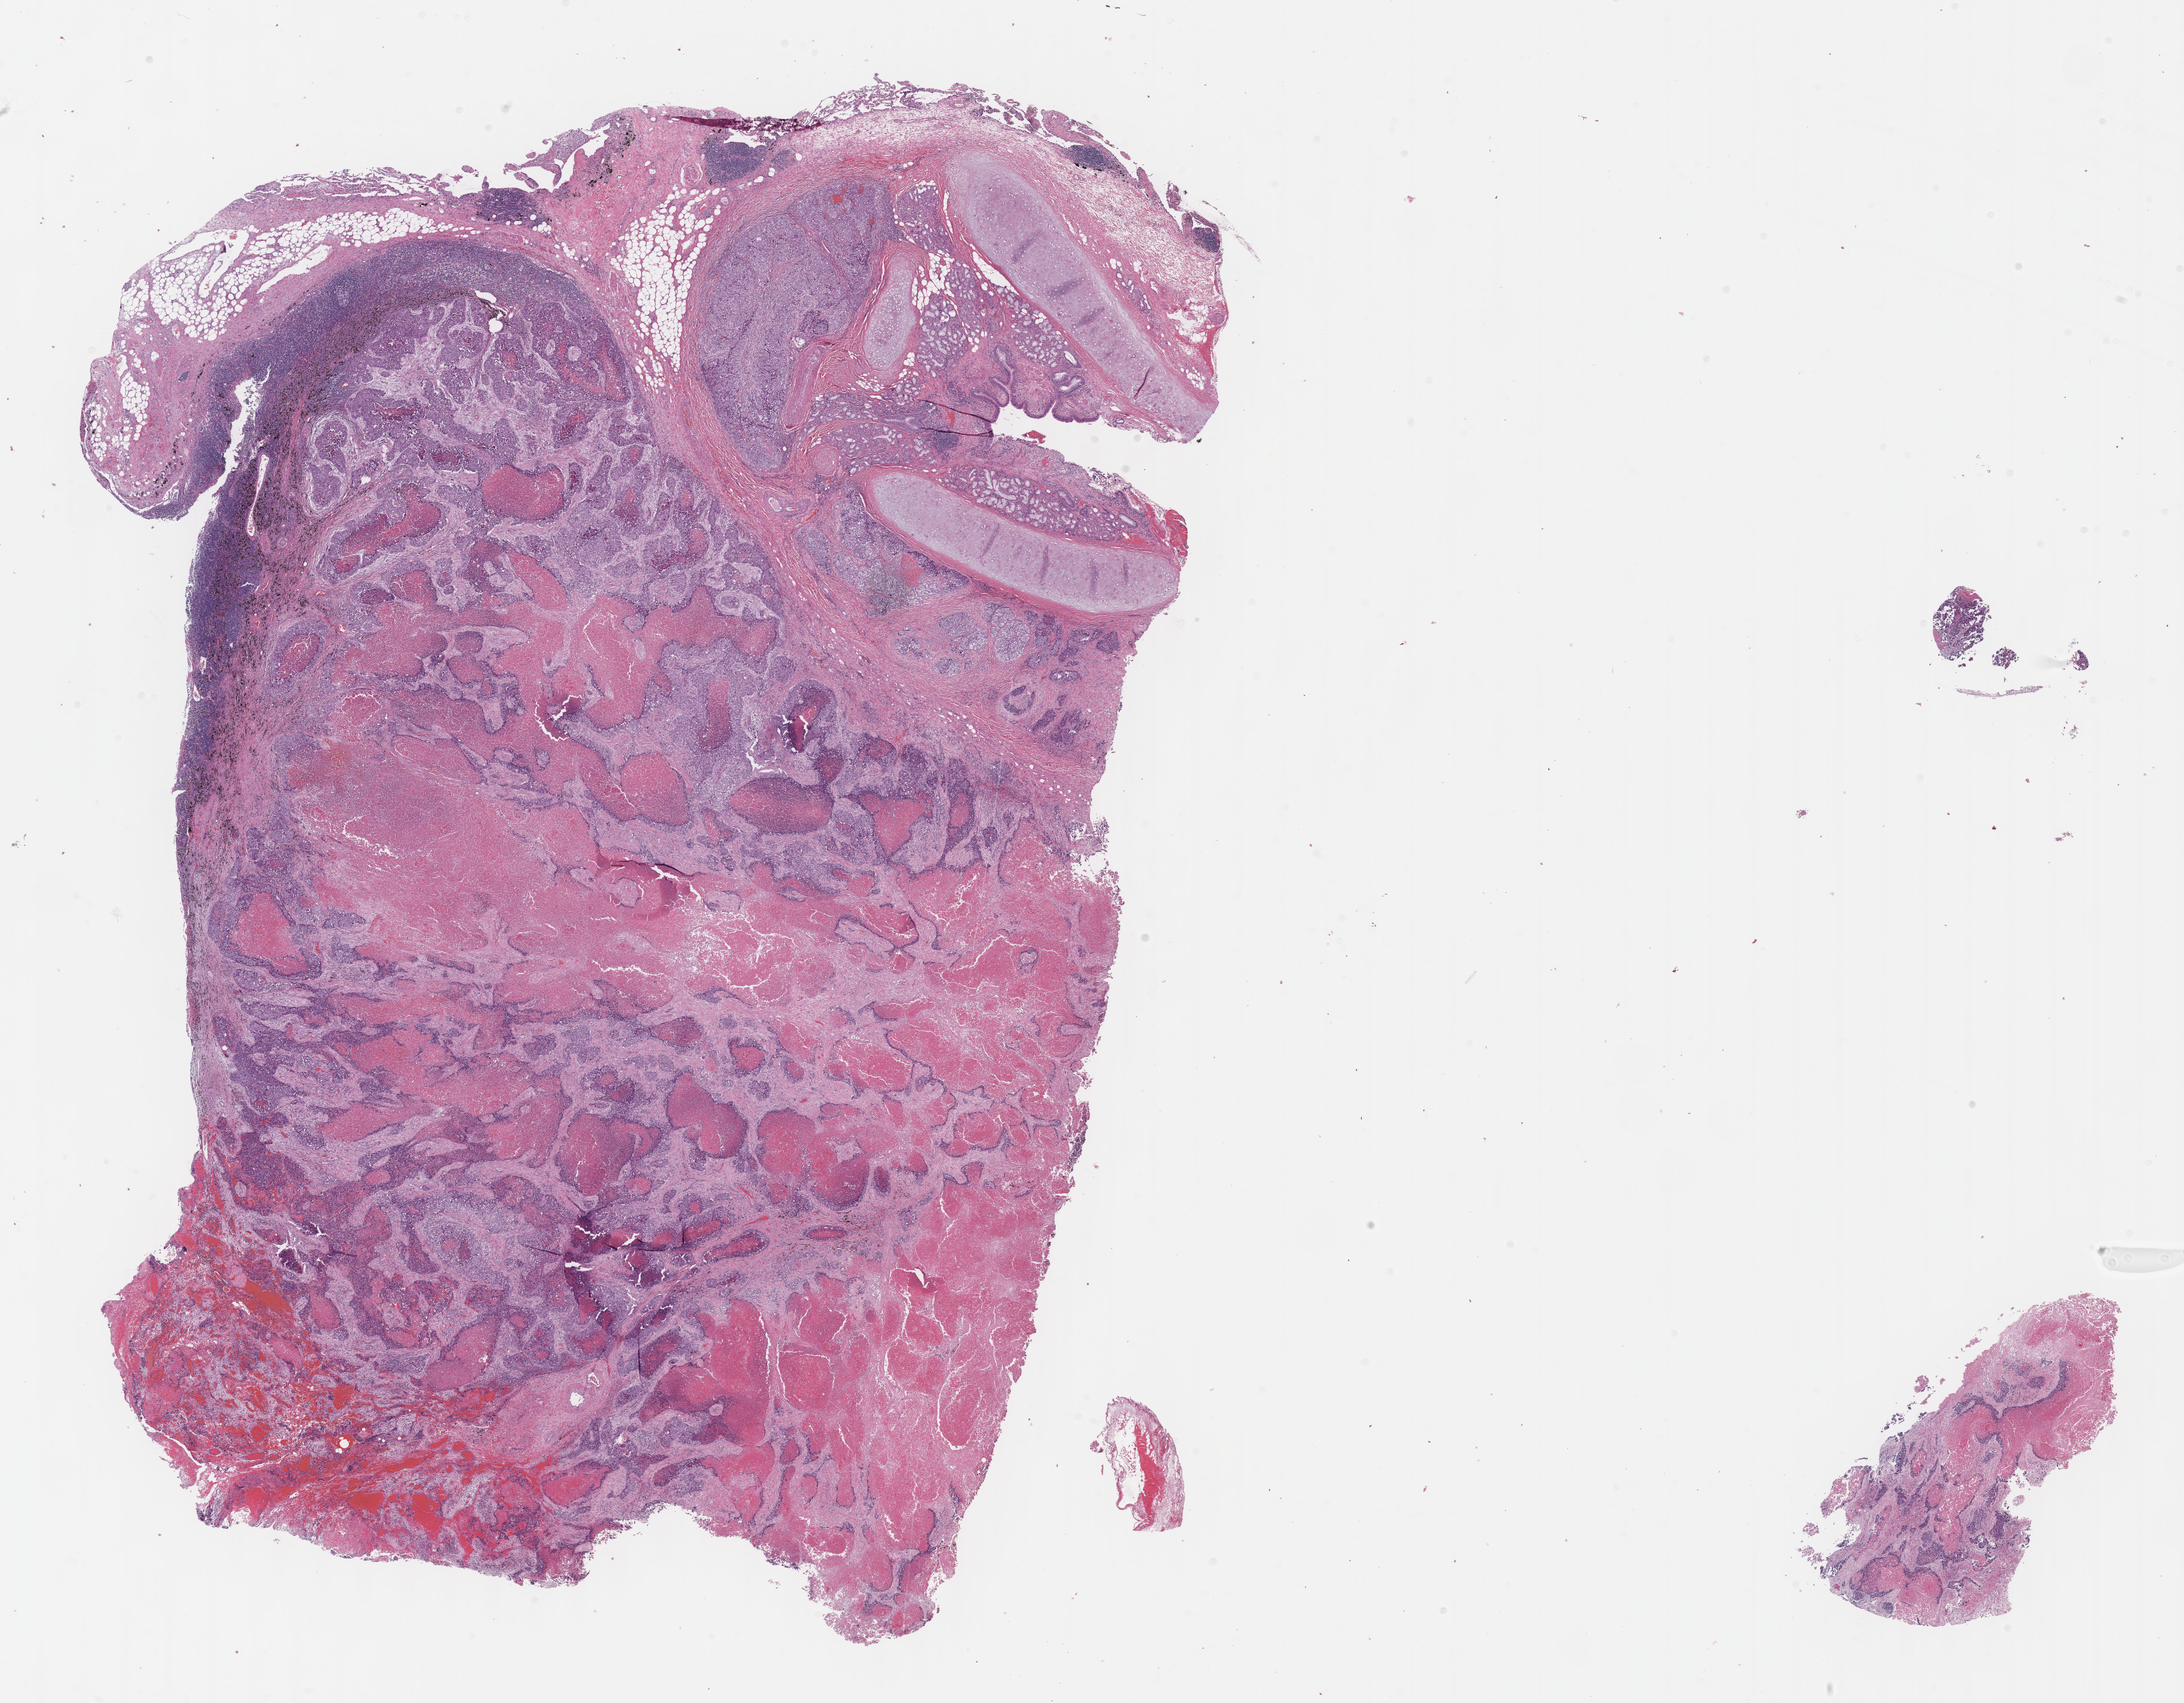
Digitized H&E-stained tissue section (whole slide), a low-resolution overview of the entire scanned area, about 25.7 x 20.0 mm; formalin-fixed paraffin-embedded (FFPE) diagnostic section; lung, primary tumour sample. Male, age 74 years at initial diagnosis.
Diagnosis: Squamous cell carcinoma, NOS (upper lobe, lung). Laterality: right. AJCC pathologic stage: IIA.